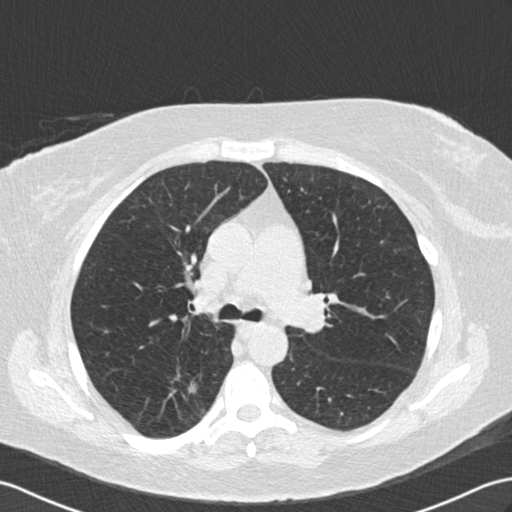
Low-dose screening chest CT, one axial slice; position 100 of 154 along the scan axis; reconstruction kernel B30f; 120 kVp; lung window (W 1500 / L -600 HU); 2 mm slice thickness; 512 × 512 image matrix, field of view 352 × 352 mm.
Structures marked on this image (expert manual segmentation):
- lesion 1 (tumor, lower lobe of right lung): bounding box <188,383,196,393> (left, top, right, bottom; pixels)